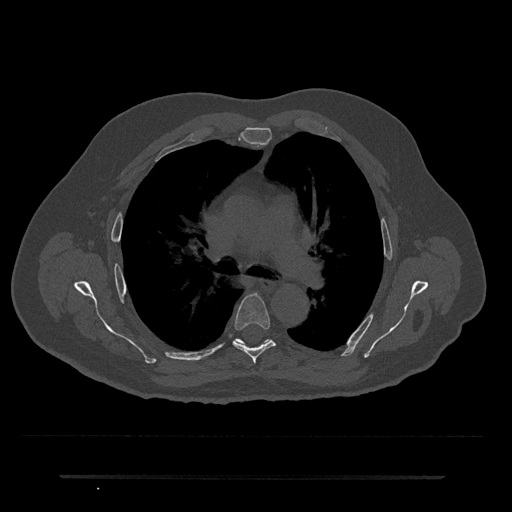
CT including the spine, one axial slice. Reconstruction kernel Br40s/3. Bone window (W 1800 / L 400 HU). 0.5 mm slice thickness. 512 × 512 image matrix, field of view 437 × 437 mm. Patient: male, 69 years. Case-level facts recorded for this patient, not image findings: primary cancer: prostate.
Annotated regions visible in this slice (semi-automatically segmented with operator editing):
- T5 vertebra: bounding box <233,294,276,364> (left, top, right, bottom; pixels)